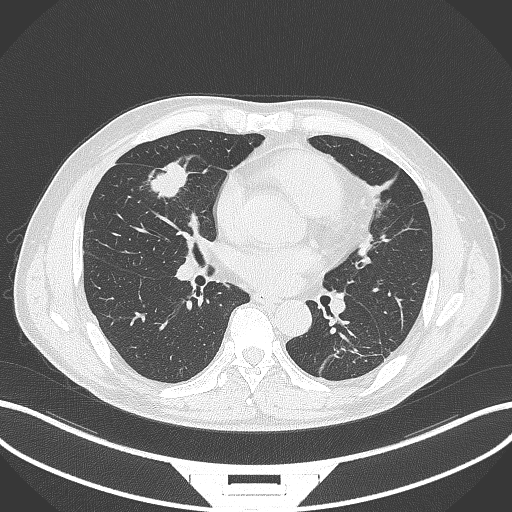
Chest CT, one axial slice; slice 143 of 399 in the series (ordered by position); reconstruction kernel B70f; lung window (W 1500 / L -600 HU); 512 × 512 image matrix, field of view 400 × 400 mm. Patient: male, 59 years. Case-level facts recorded for this patient, not image findings: clinical TNM (as recorded): T2a N1 M0.
Structures marked on this image (rectangle marked by the reading radiologist):
- lung tumour (recorded histology: adenocarcinoma): bounding box [x1, y1, x2, y2] px = [144, 158, 190, 202]